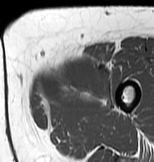
MRI of an extremity soft-tissue mass, one axial slice; position 18 of 83 along the scan axis; MR volume resampled by the dataset authors to the PET/CT grid (not the native acquisition matrix); 3.27 mm slice thickness; 154 × 162 image matrix, field of view 150 × 158 mm. Female patient. From the clinical record (not read from this slice): histological type: myxofibrosarcoma; grade: intermediate; site of the primary tumour: left thigh.
Outlined on this slice (expert contour drawn on MRI and transferred to this co-registered scan by the dataset authors):
- gross tumour volume including surrounding oedema: bounding box [x1, y1, x2, y2] px = [35, 55, 111, 119]
- gross tumour volume (mass): [39, 59, 107, 119]